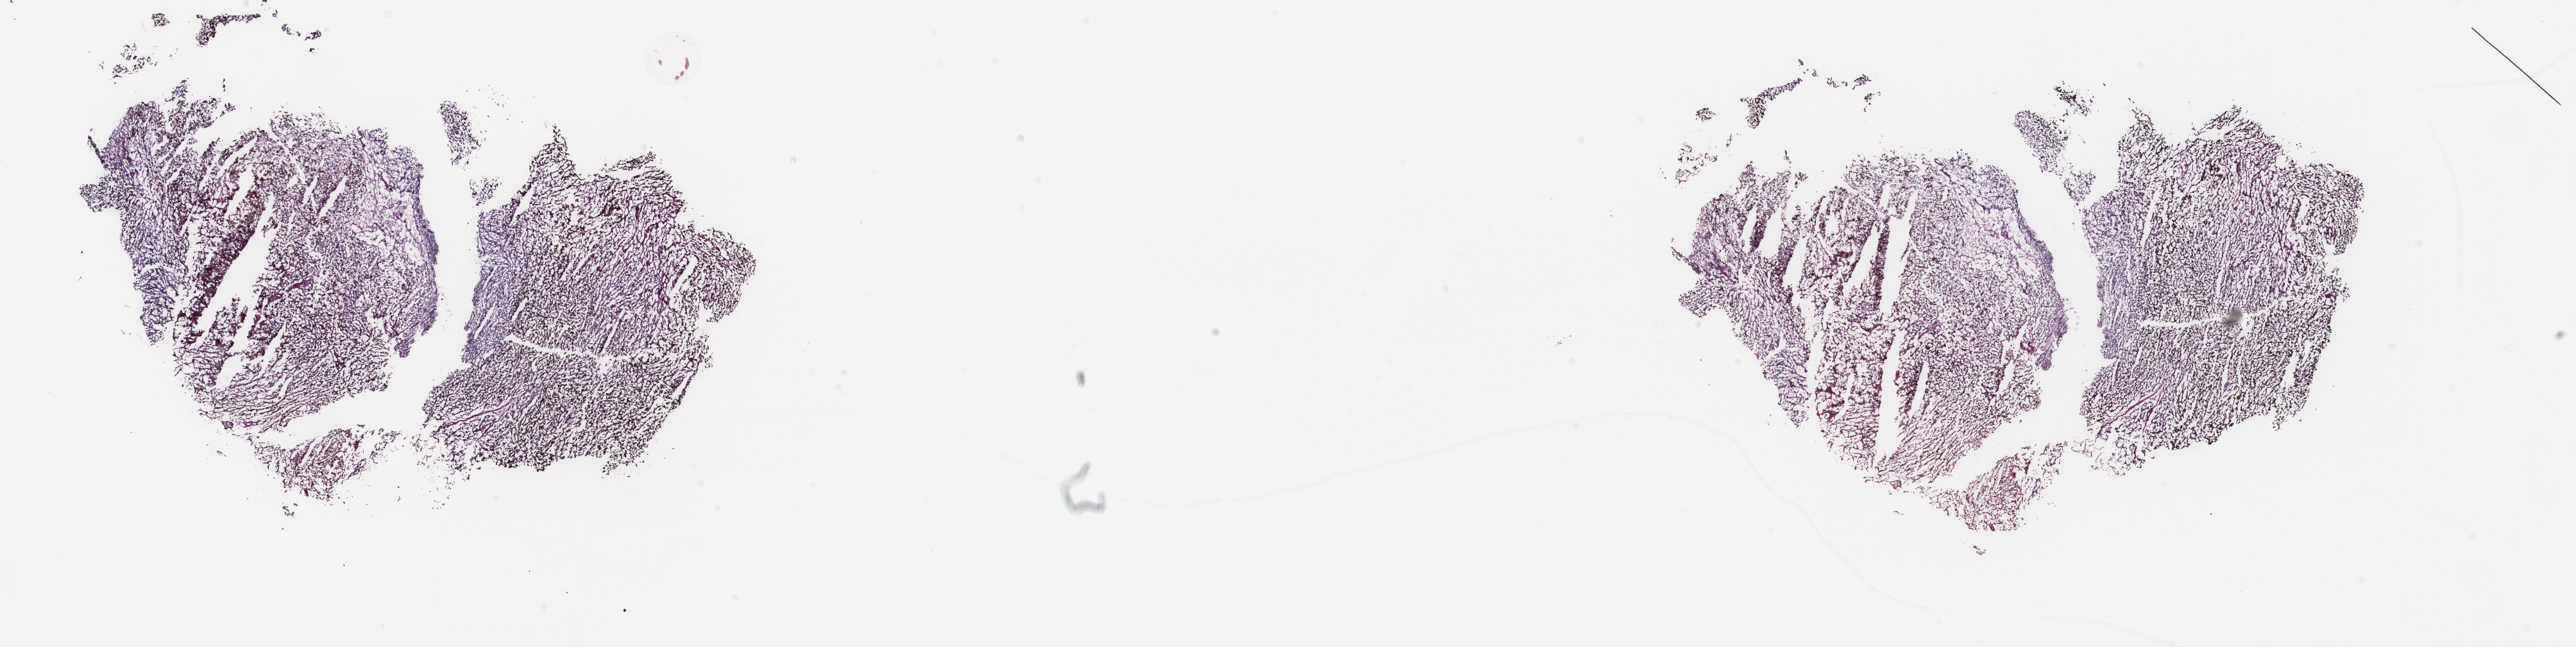
Whole-slide histology image, H&E — a low-resolution overview of the entire scanned area, about 31.9 x 8.0 mm (acquisition: 40x scan). Frozen section from the top of the tissue portion. Metastatic tumour sample, sampled site not recorded. Patient: male, age at initial diagnosis 63 years. Pathologist review of this section (percent, as recorded): tumour cells 90%, tumour nuclei 90%, normal cells 0%, stromal cells 10%, necrosis 0%. Inflammatory infiltration, as recorded: lymphocyte infiltration 3%, monocyte infiltration 0%, neutrophil infiltration 0%.
This section: metastatic tumour tissue. Patient diagnosis: Malignant melanoma, NOS.